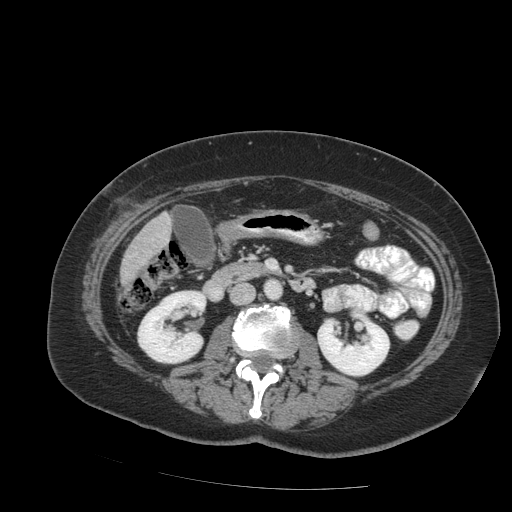
Contrast-enhanced abdominal CT (liver protocol), one axial slice; soft-tissue window (W 400 / L 40 HU); 512 × 512 image matrix, field of view 400 × 400 mm. From the clinical record (not read from this slice): diagnosis: hepatocellular carcinoma (patient treated with transarterial chemoembolisation; whether this scan precedes or follows treatment is not stated here); TNM stage (as recorded): Stage-IVB; Child-Pugh class: A.
Outlined on this slice (semi-automatically segmented with operator editing):
- liver parenchyma outside the tumour (the mass and vessels are separate outlines, so this box may not span the whole liver): box from (x=120, y=212) to (x=170, y=286) px